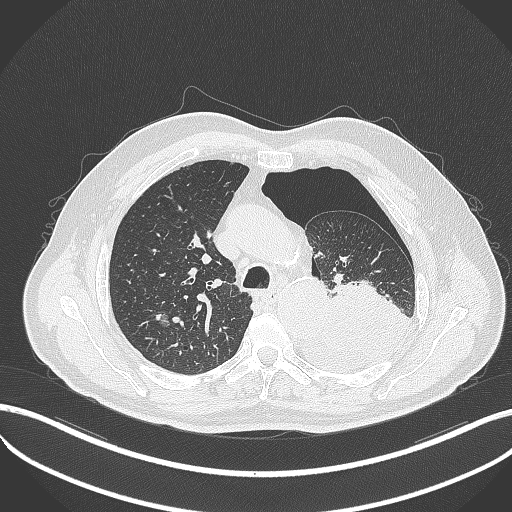
Chest CT, one axial slice. Slice 364 of 464 in the series (ordered by position). Reconstruction kernel B70f. 120 kVp. Lung window (W 1500 / L -600 HU). 1 mm slice thickness. 512 × 512 image matrix, field of view 400 × 400 mm. Patient: male, 76 years. Case-level facts recorded for this patient, not image findings: clinical TNM (as recorded): T3 N0 M1b.
Annotated regions visible in this slice (bounding box drawn by a radiologist):
- lung tumour (recorded histology: adenocarcinoma): bounding box <298,279,412,371> (left, top, right, bottom; pixels)